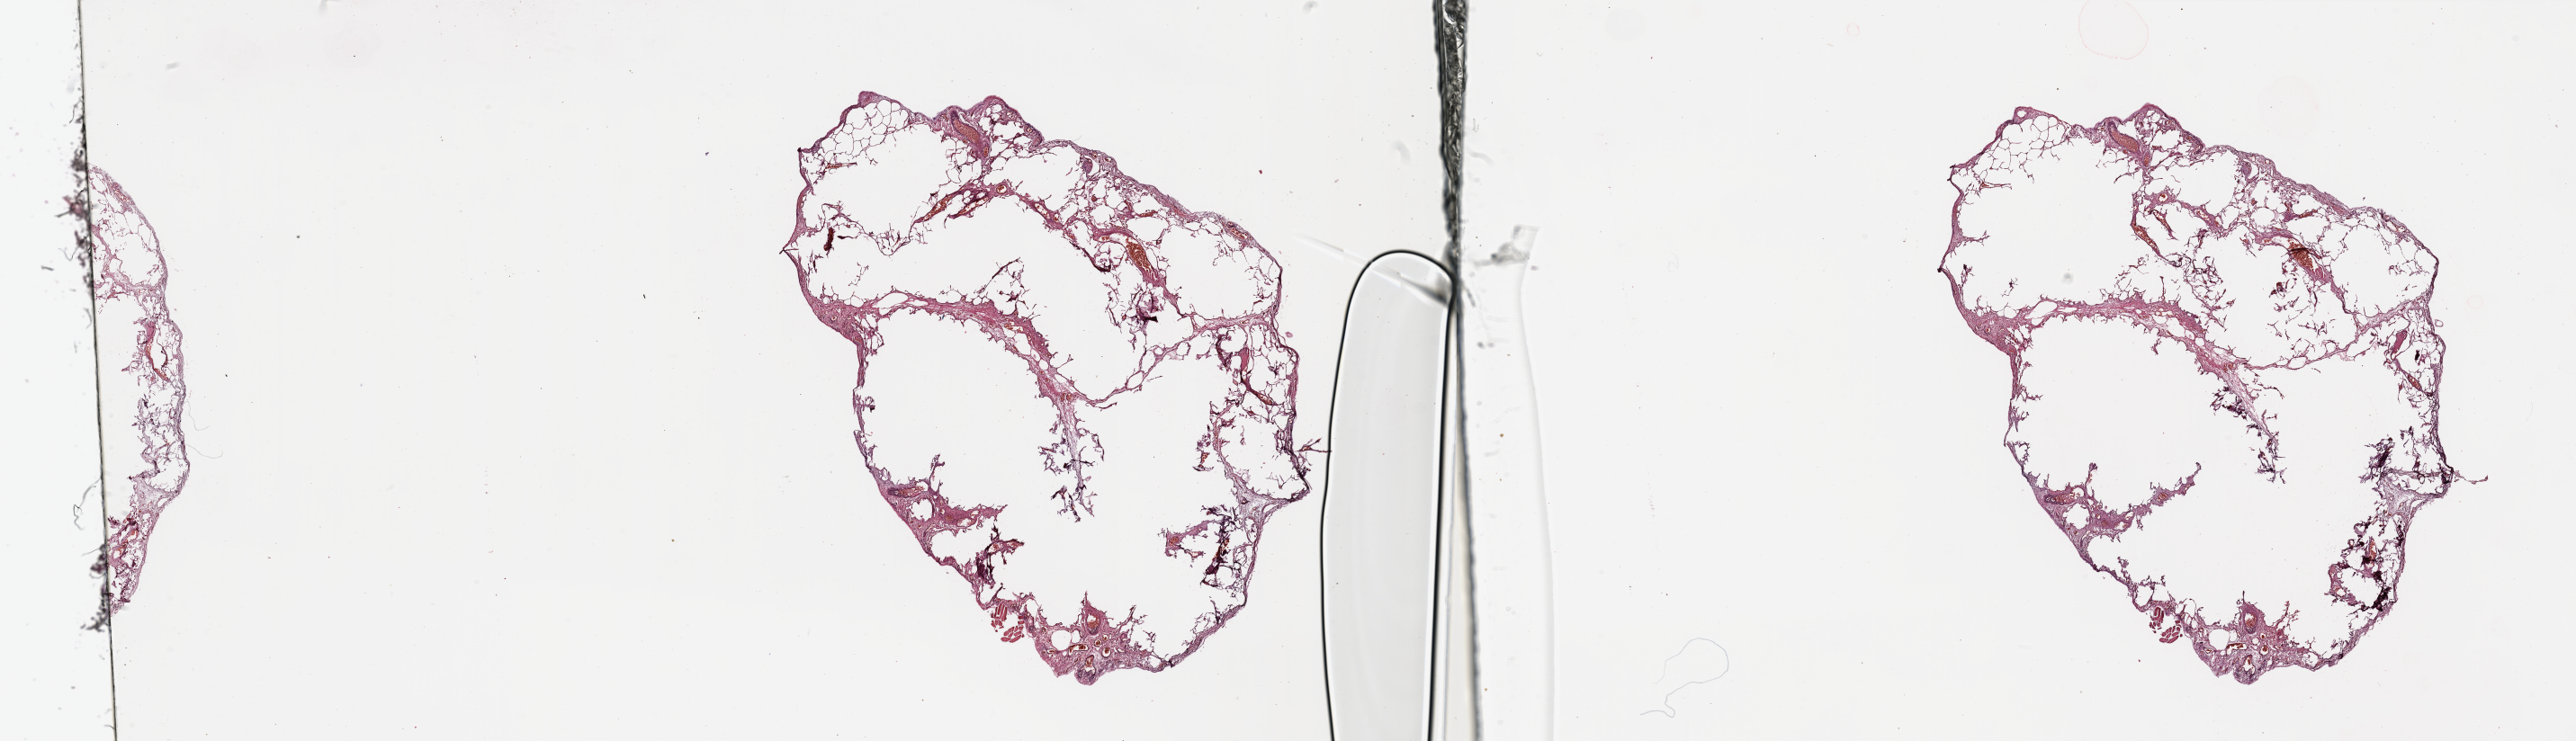
Hematoxylin and eosin (H&E) stained whole-slide image — low-resolution overview of the scanned area, about 45.3 x 13.0 mm. Normal (non-tumour) tissue sample, sampled site: lung. Male, 78 y/o.
- this section: normal (non-tumour) tissue from the same patient
- patient diagnosis: Squamous cell carcinoma, NOS